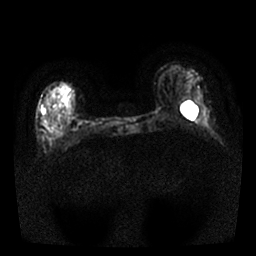
Breast MRI, one axial slice; diffusion-weighted series; image 2 of 4 stored at this slice position (different b-values; order by instance number); 1.5 T; 4 mm slice thickness; 256 × 256 image matrix, field of view 310 × 310 mm. Female patient.
Outlined on this slice (expert manual segmentation):
- tumour on diffusion-weighted imaging: box from (x=41, y=109) to (x=45, y=114) px